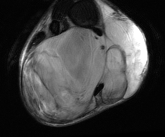
MRI of an extremity soft-tissue mass, one axial slice; position 27 of 81 along the scan axis; T2-weighted fat-saturated; MR volume resampled by the dataset authors to the PET/CT grid (not the native acquisition matrix); 3.27 mm slice thickness; 165 × 137 image matrix. Male patient. From the clinical record (not read from this slice): histological type: liposarcoma - round cell; grade: high; site of the primary tumour: right calf.
Annotated regions visible in this slice (expert contour drawn on MRI and transferred to this co-registered scan by the dataset authors):
- gross tumour volume (mass): bounding box [x1, y1, x2, y2] px = [21, 18, 147, 119]